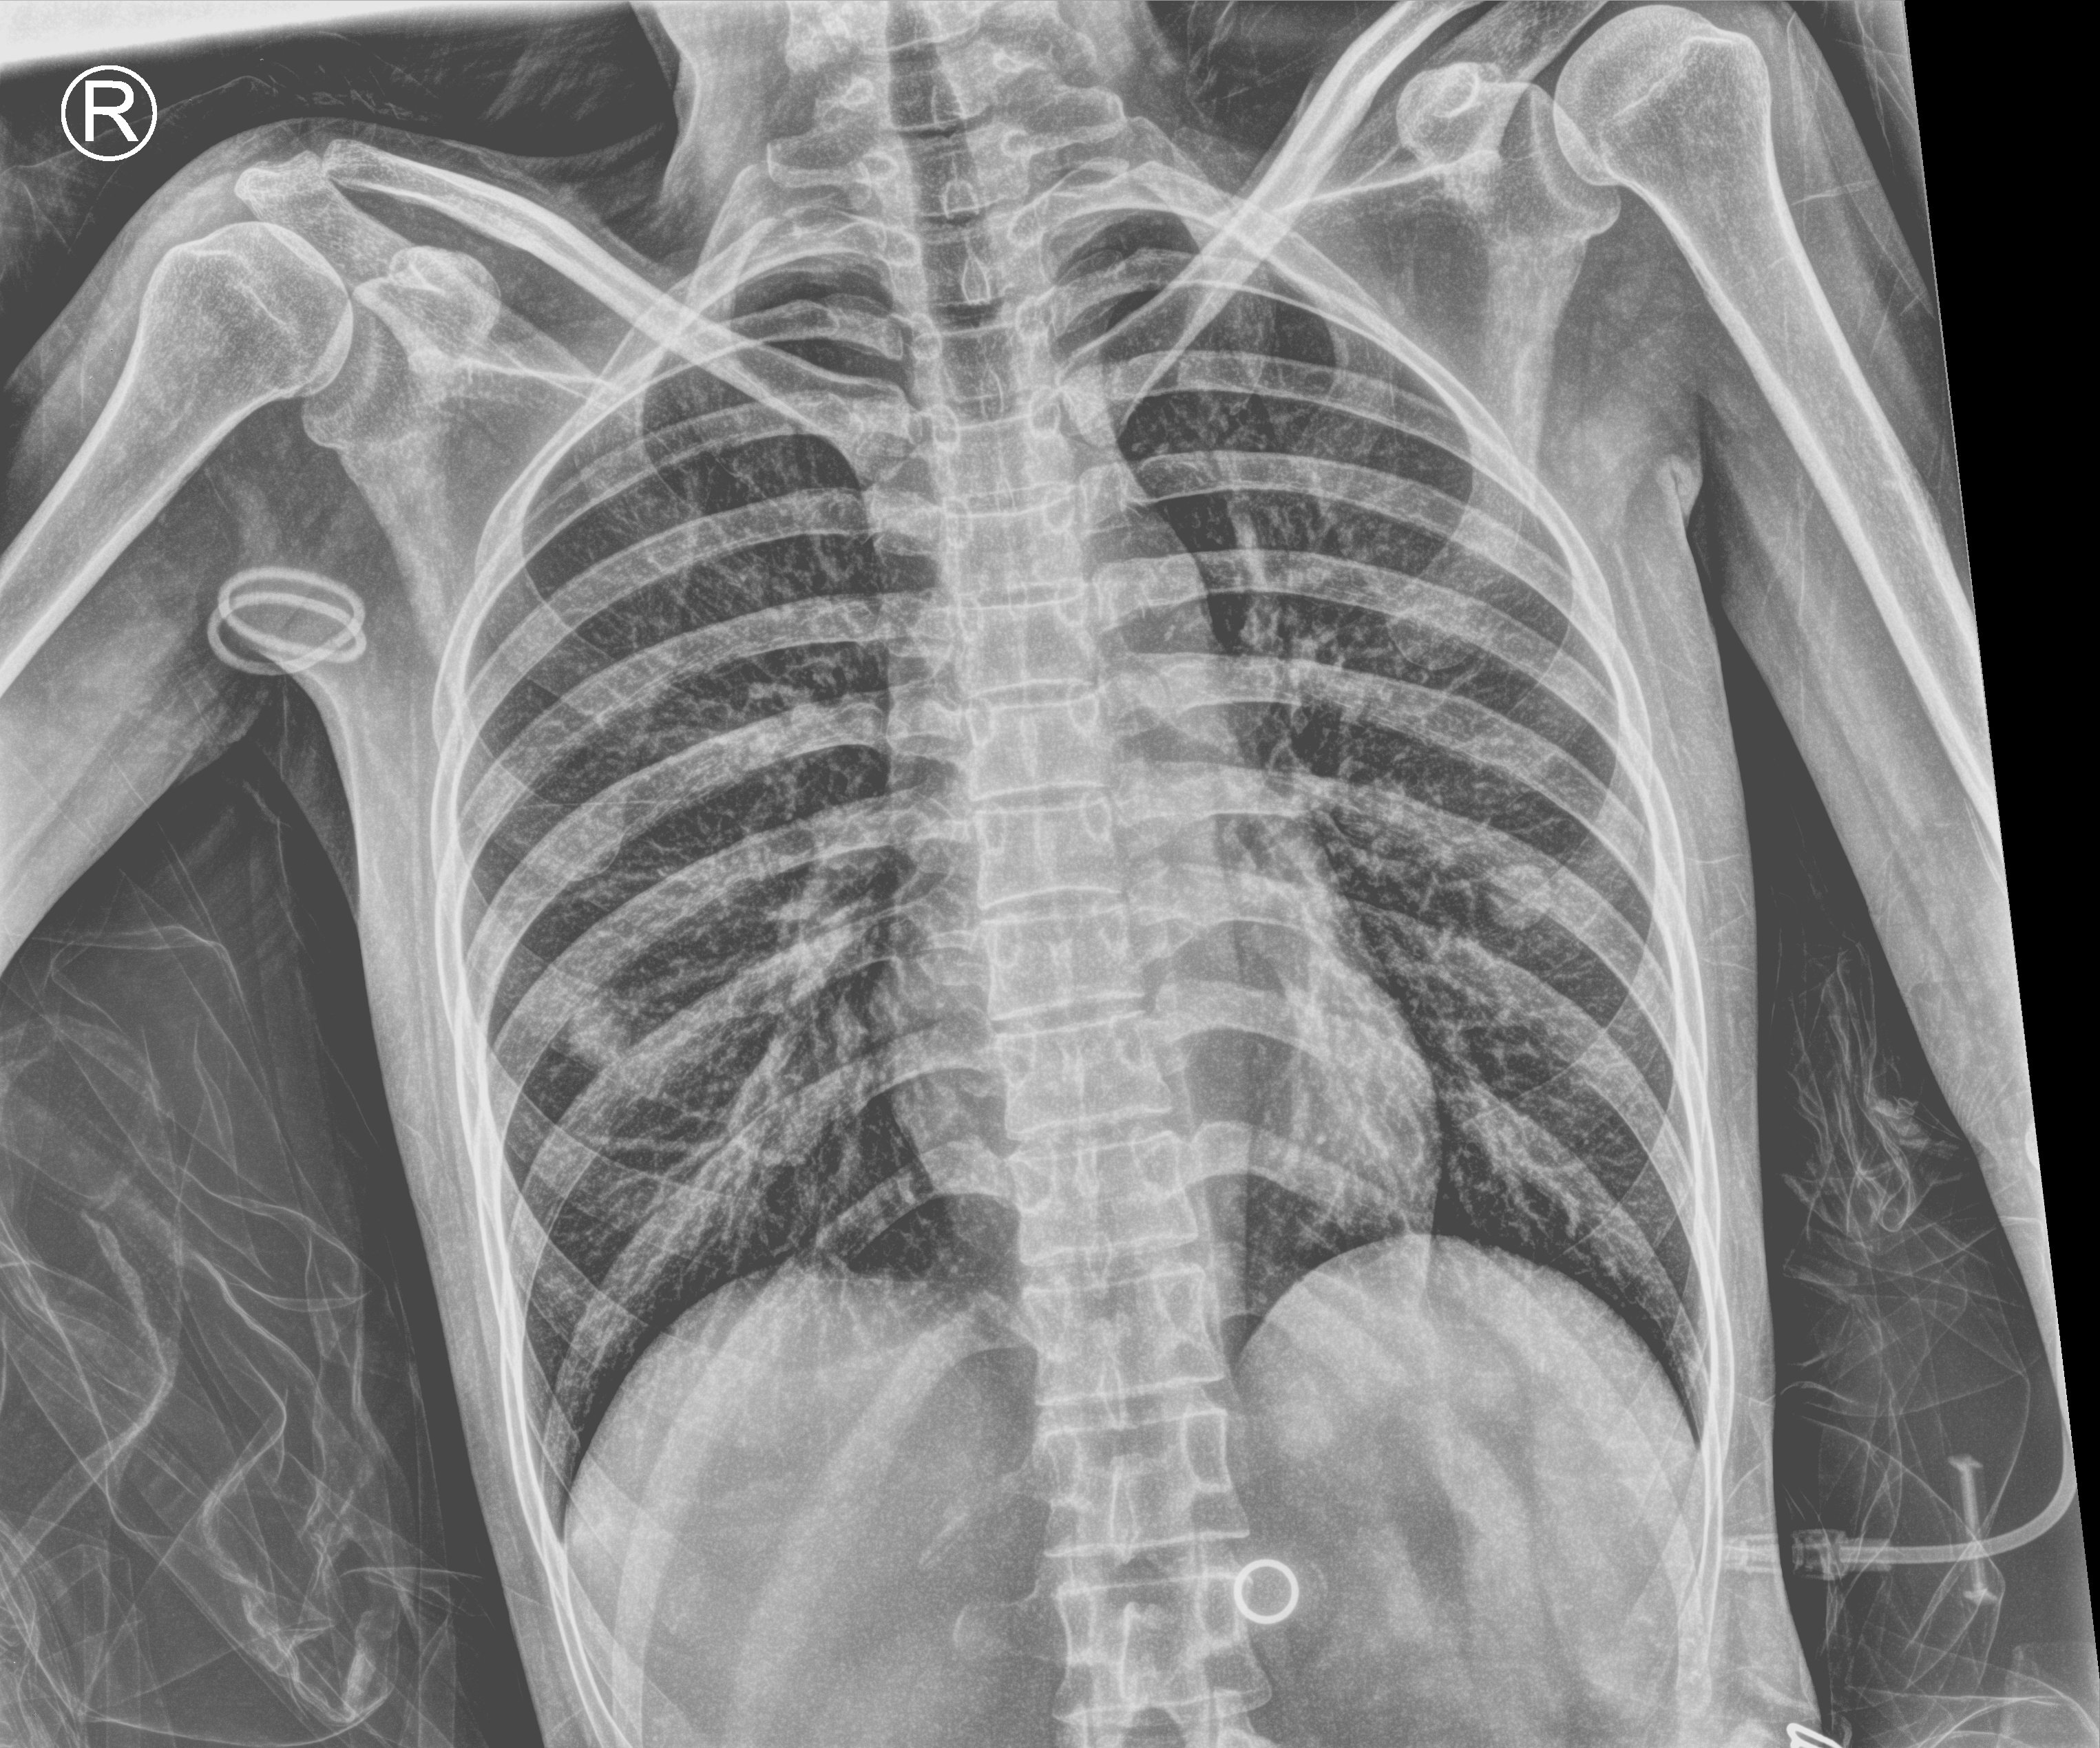
Portable chest radiograph, anteroposterior (AP) projection. Patient hospitalised with COVID-19; female, aged 18–59 years.
Admission-level facts for this patient (not findings on this image; timing relative to this image not recorded): admitted to intensive care during this hospital stay: no; smoking status (admission record): never; mechanically ventilated during this hospital stay: no.